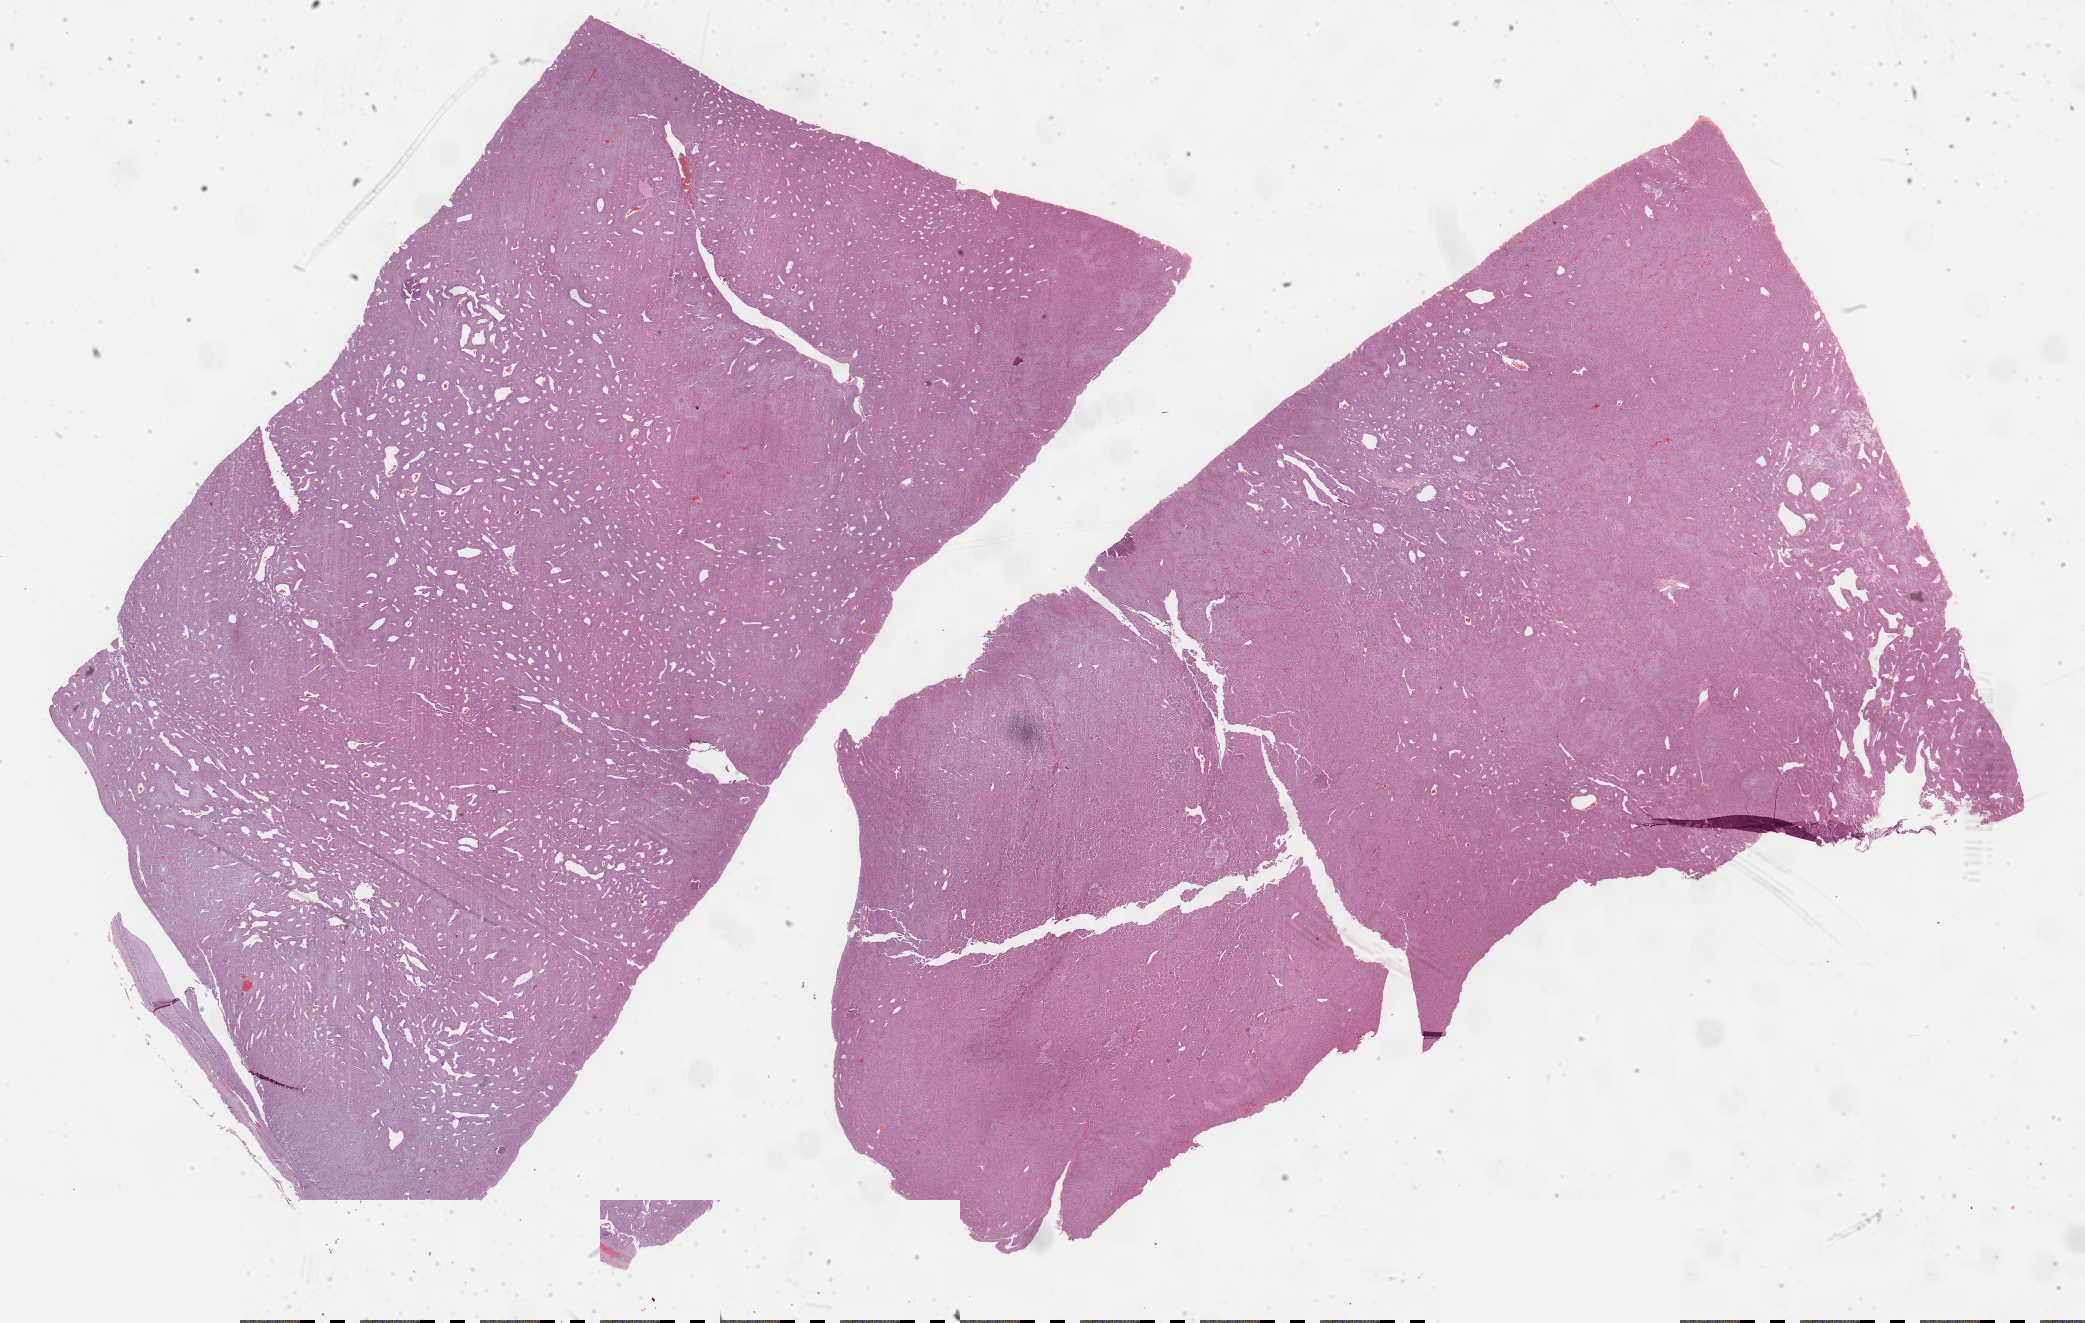
Digitized Hematoxylin and eosin (H&E) stained tissue section (whole slide), shown as a low-resolution overview of the whole scanned area (about 33.7 x 21.4 mm, acquisition: 40x scan), FFPE section, sample: primary tumour, adrenal cortex. Male, age 47 years at initial diagnosis.
• diagnosis: Adrenal cortical carcinoma (cortex of adrenal gland)